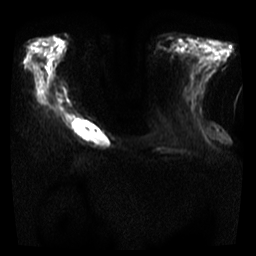
Breast MRI, one axial slice. Slice 11 of 35 in the series (ordered by position). Diffusion-weighted series; image 2 of 4 stored at this slice position (different b-values; order by instance number). 3 T. 256 × 256 image matrix, field of view 300 × 300 mm. Female patient.
Annotated regions visible in this slice (manually delineated by an expert):
- tumour on diffusion-weighted imaging: bounding box <70,119,110,147> (left, top, right, bottom; pixels)